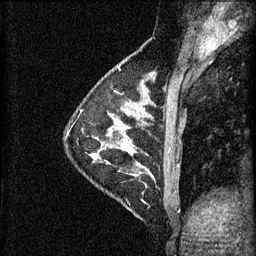
Breast MRI (dynamic contrast-enhanced), one sagittal slice; 3 images stored at this slice position (order not interpretable as contrast timing); 1.5 T; TE 4.2 ms, TR 11 ms; 2 mm slice thickness; 256 × 256 image matrix, field of view 180 × 180 mm. Patient: female, 29 years.
Structures marked on this image (semi-automatically segmented with operator editing):
- analysis volume of interest (the breast-tissue region the enhancement analysis was run in; not a lesion): bounding box (x1, y1, x2, y2) in pixels: (112, 172, 171, 223)
- tumour enhancement mask (voxels above the 70 % enhancement threshold inside the analysis volume of interest): (140, 172, 154, 179)